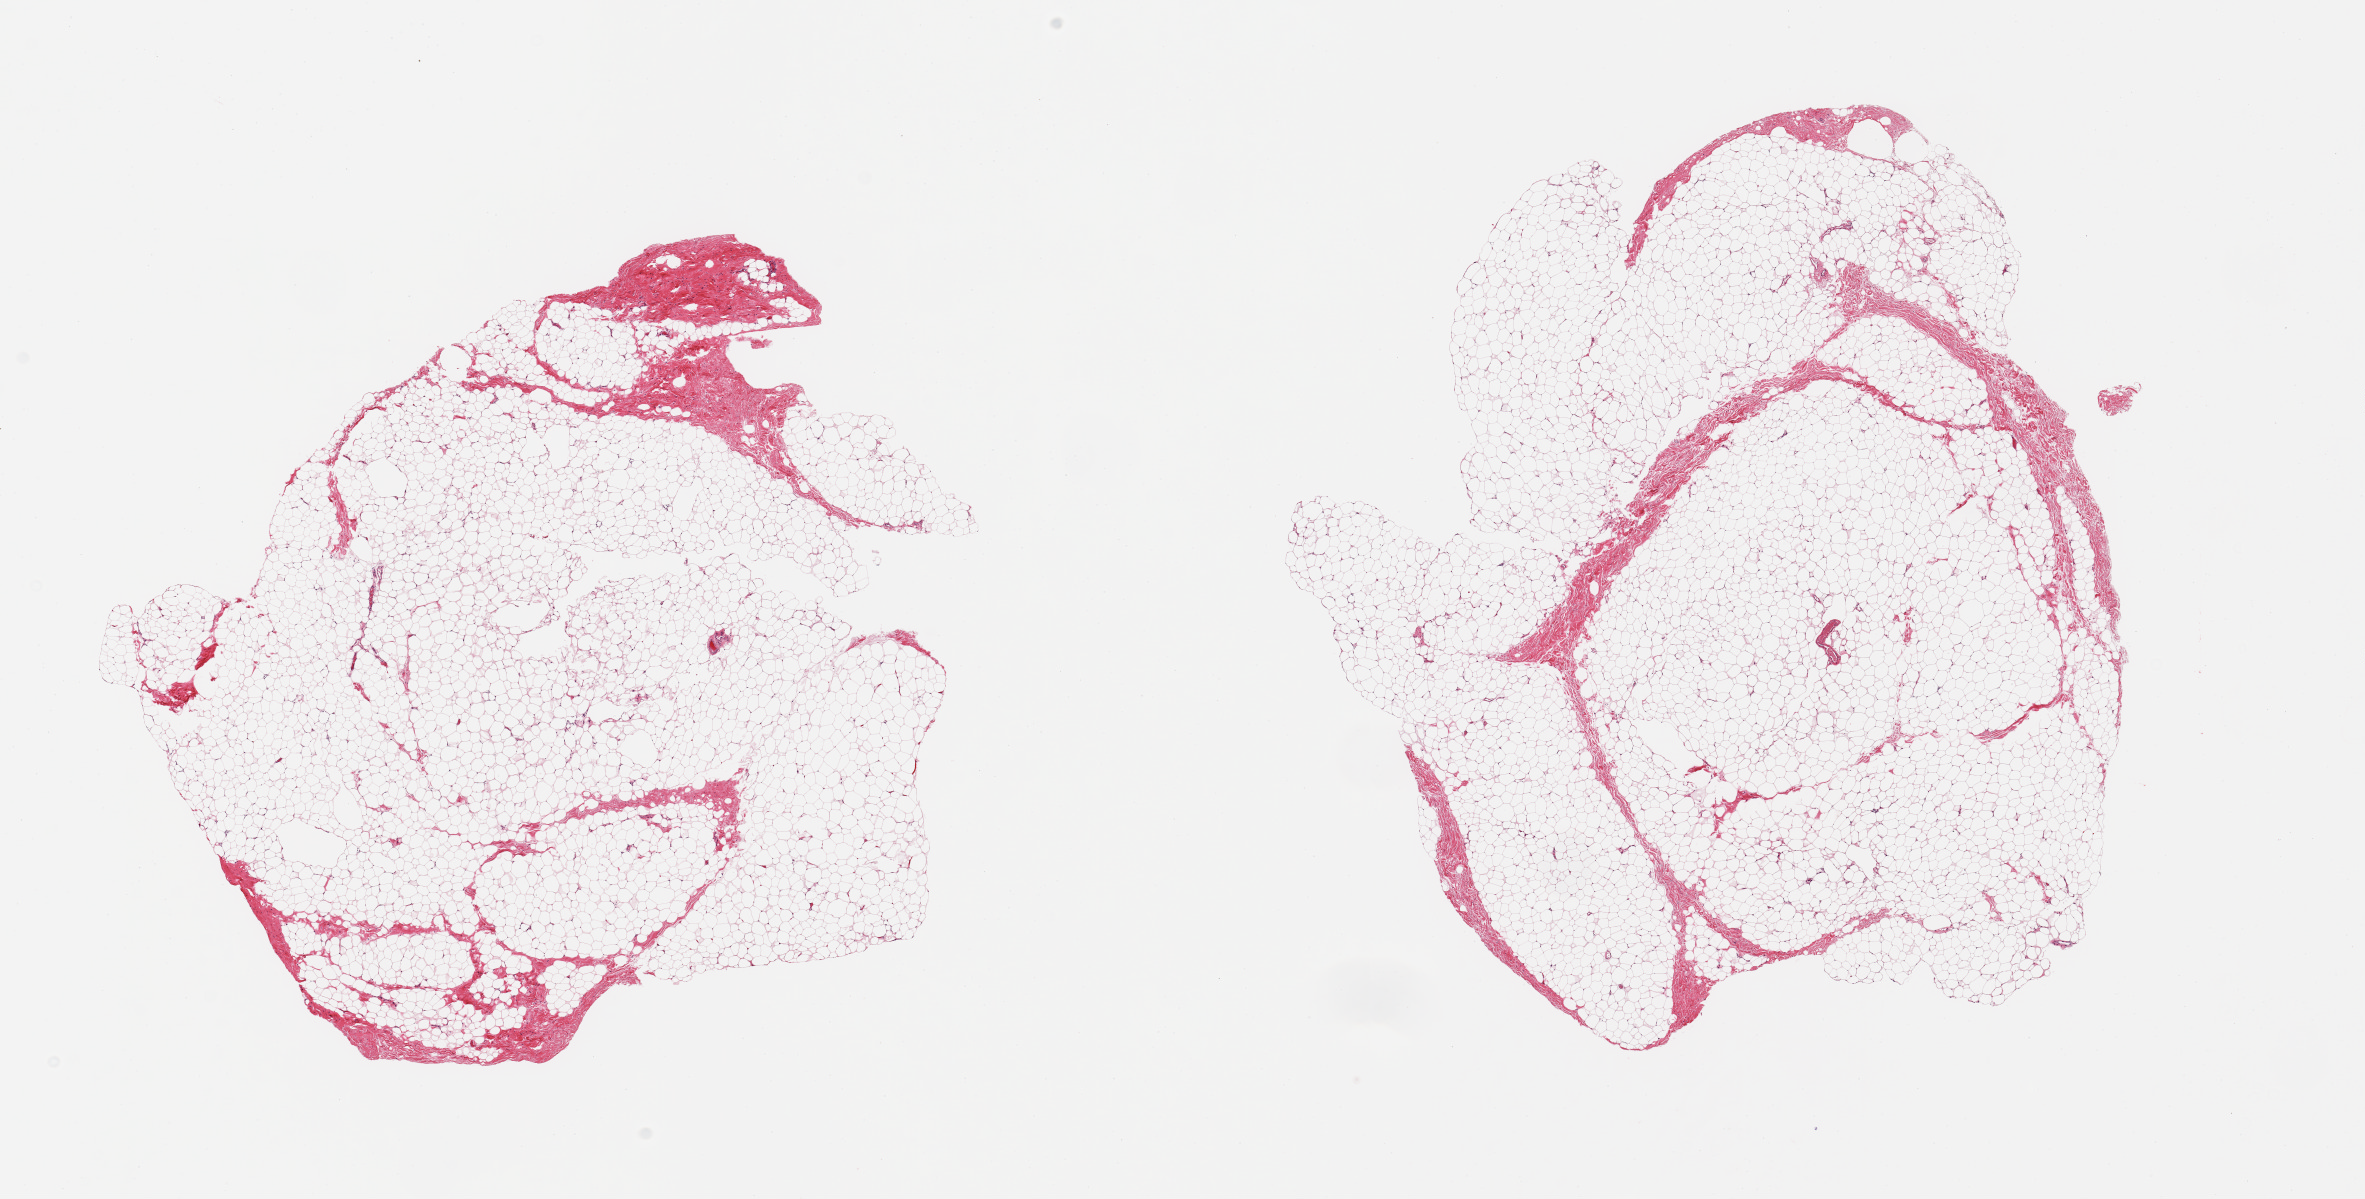
Haematoxylin and eosin whole-slide image, shown as a low-resolution overview of the whole scanned area (about 18.7 x 9.5 mm, from a 20x scan). PAXgene-fixed paraffin-embedded (PFPE) section. Target tissue: breast. Donor tissue sample. Male donor.
Reviewer comment on this tissue sample: 2 pieces, fibroadipose elements only.